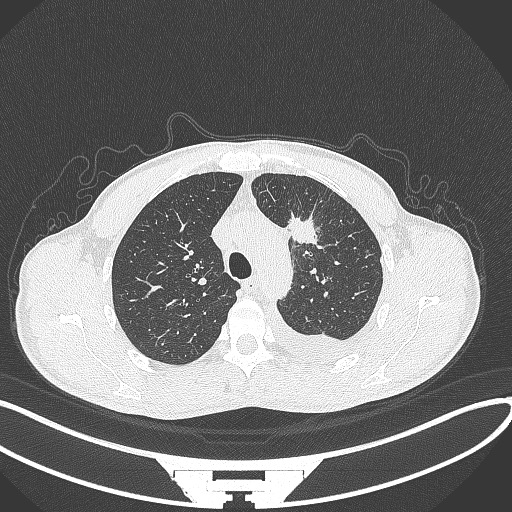
Chest CT, one axial slice; position 253 of 371 along the scan axis; 120 kVp; lung window (W 1500 / L -600 HU); 1 mm slice thickness; 512 × 512 image matrix. Patient: male, 49 years. Case-level facts recorded for this patient, not image findings: clinical TNM (as recorded): T1c N1 M1.
Structures marked on this image (bounding box drawn by a radiologist):
- lung tumour (recorded histology: adenocarcinoma): box from (x=287, y=211) to (x=319, y=253) px